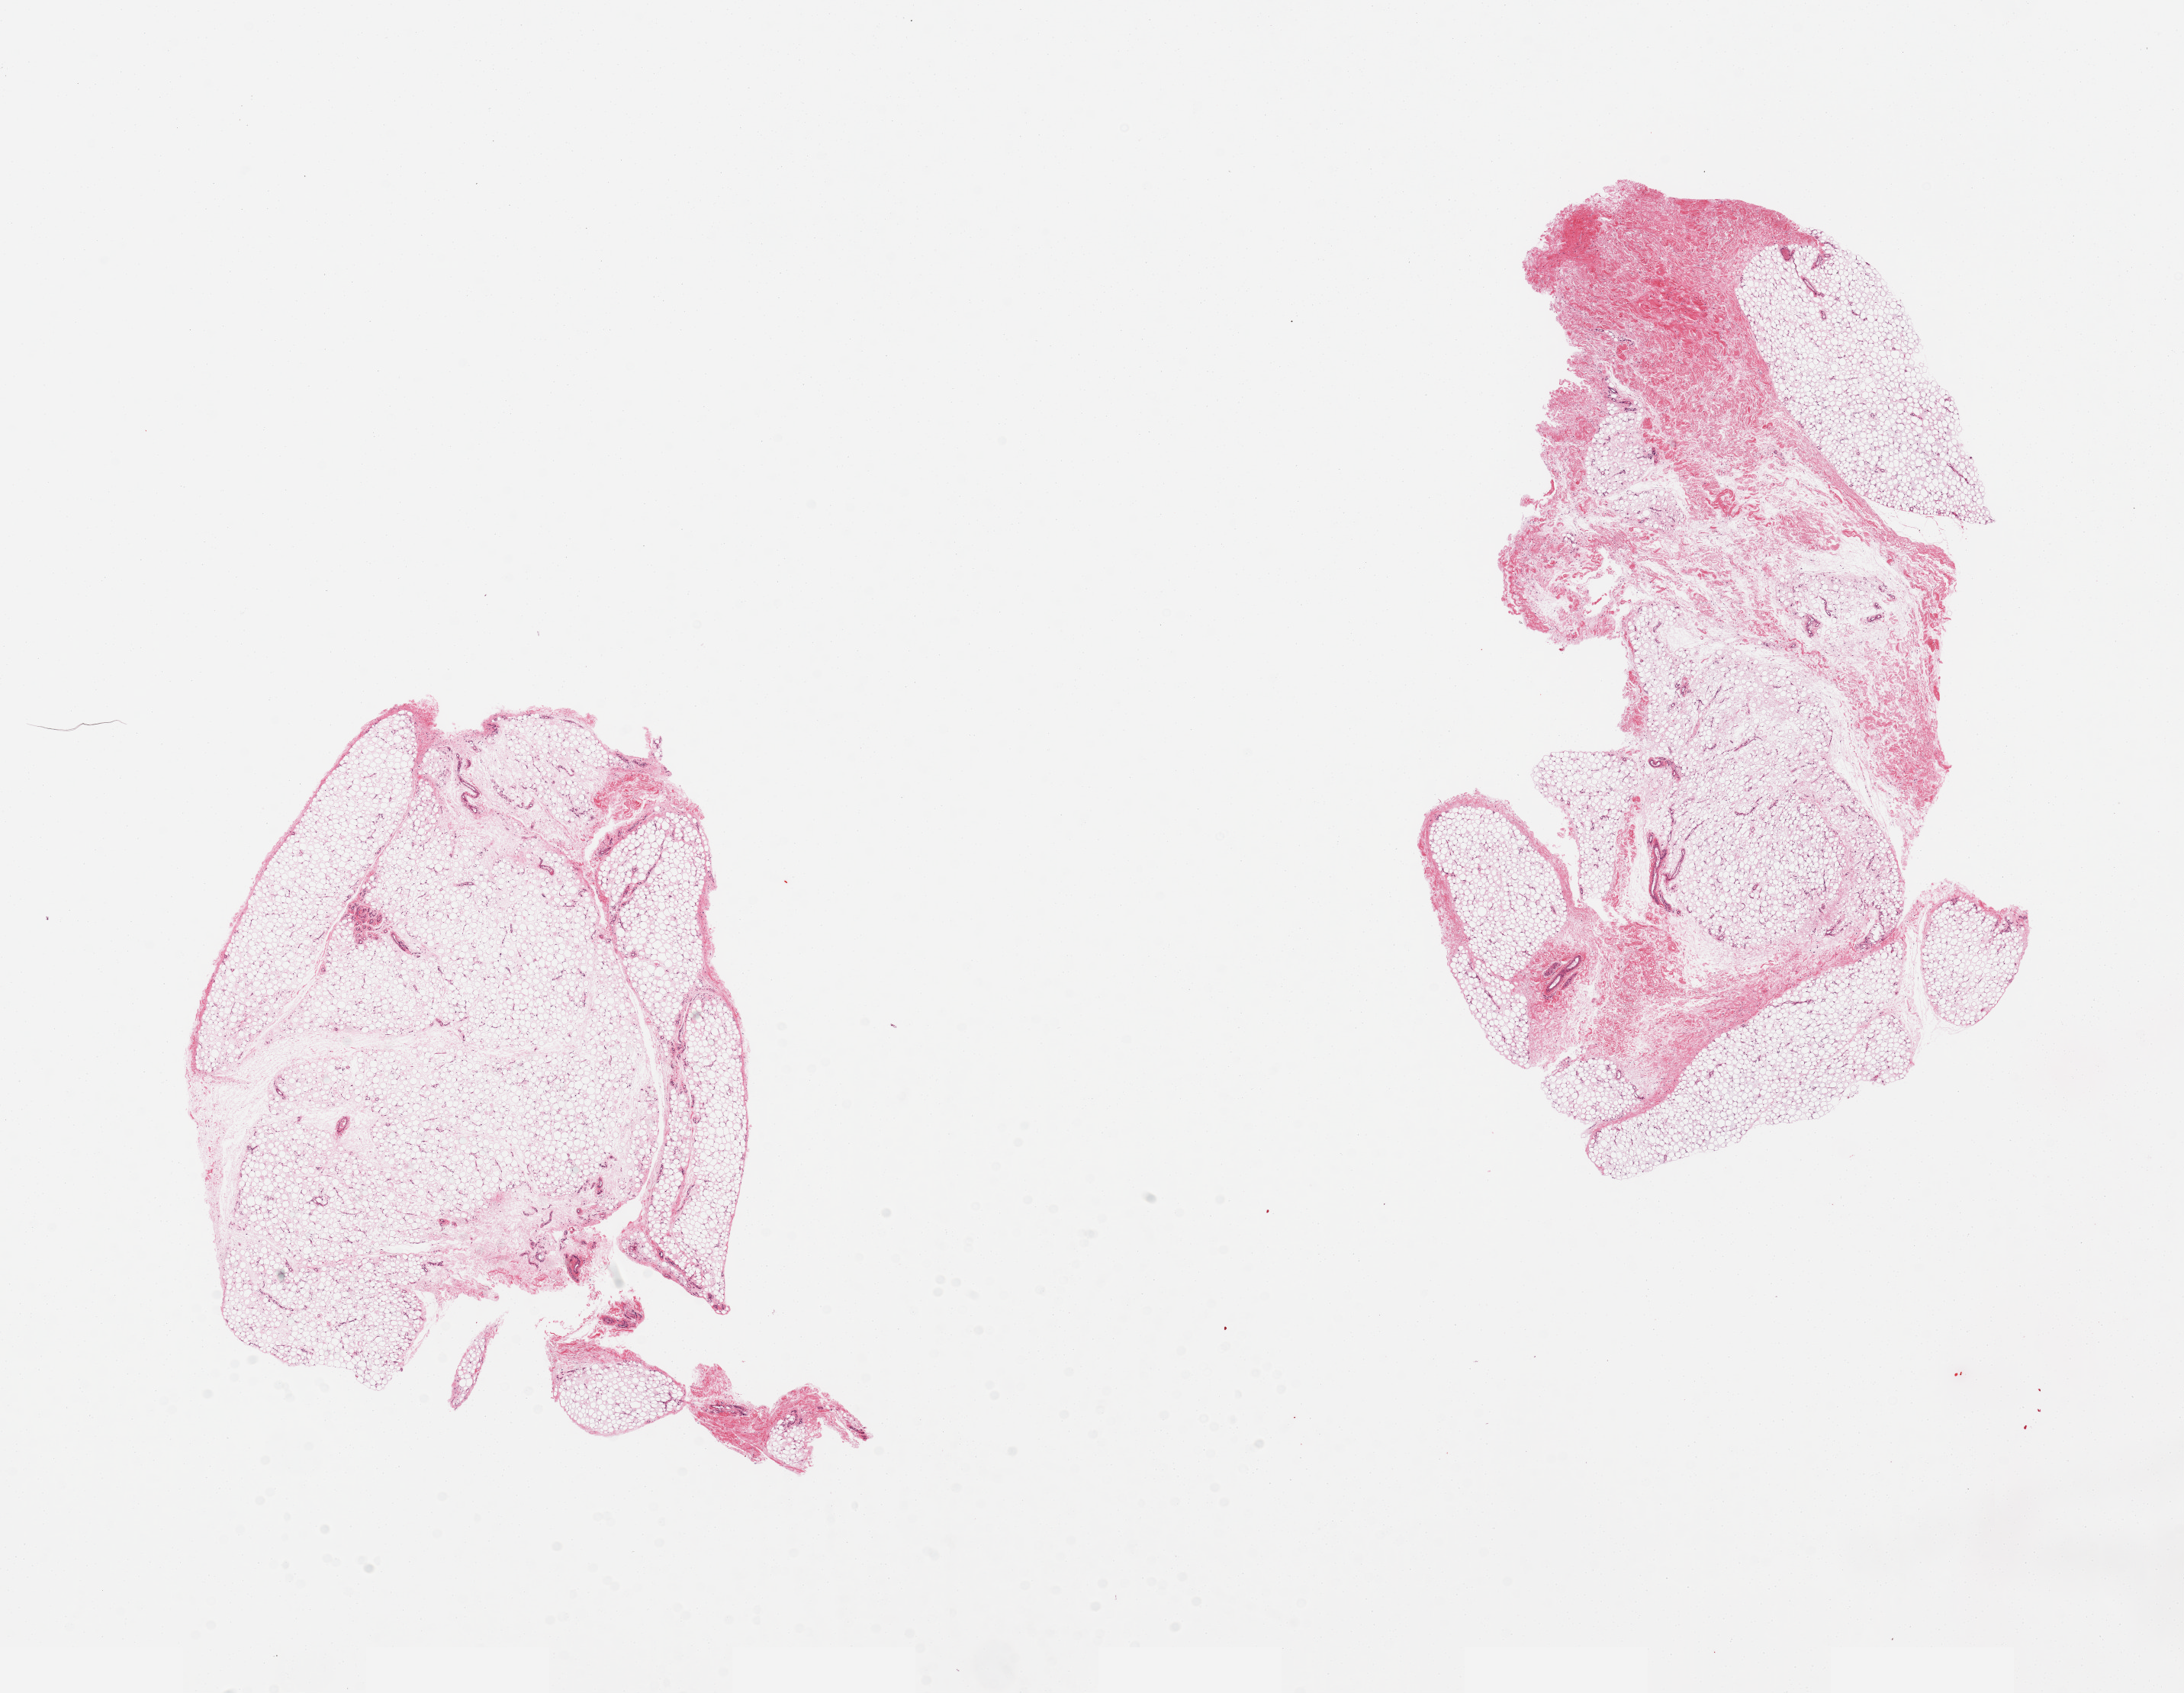
Whole-slide image, H&E stain, brightfield — low-resolution overview of the scanned area, about 22.6 x 17.6 mm (acquisition: 20x scan), PAXgene-fixed paraffin-embedded (PFPE) section, sampled site (target tissue): adipose tissue, donor tissue sample. Donor sex: male.
Review note (as recorded): 2 pieces, 1 with 20% fibrous tissue.